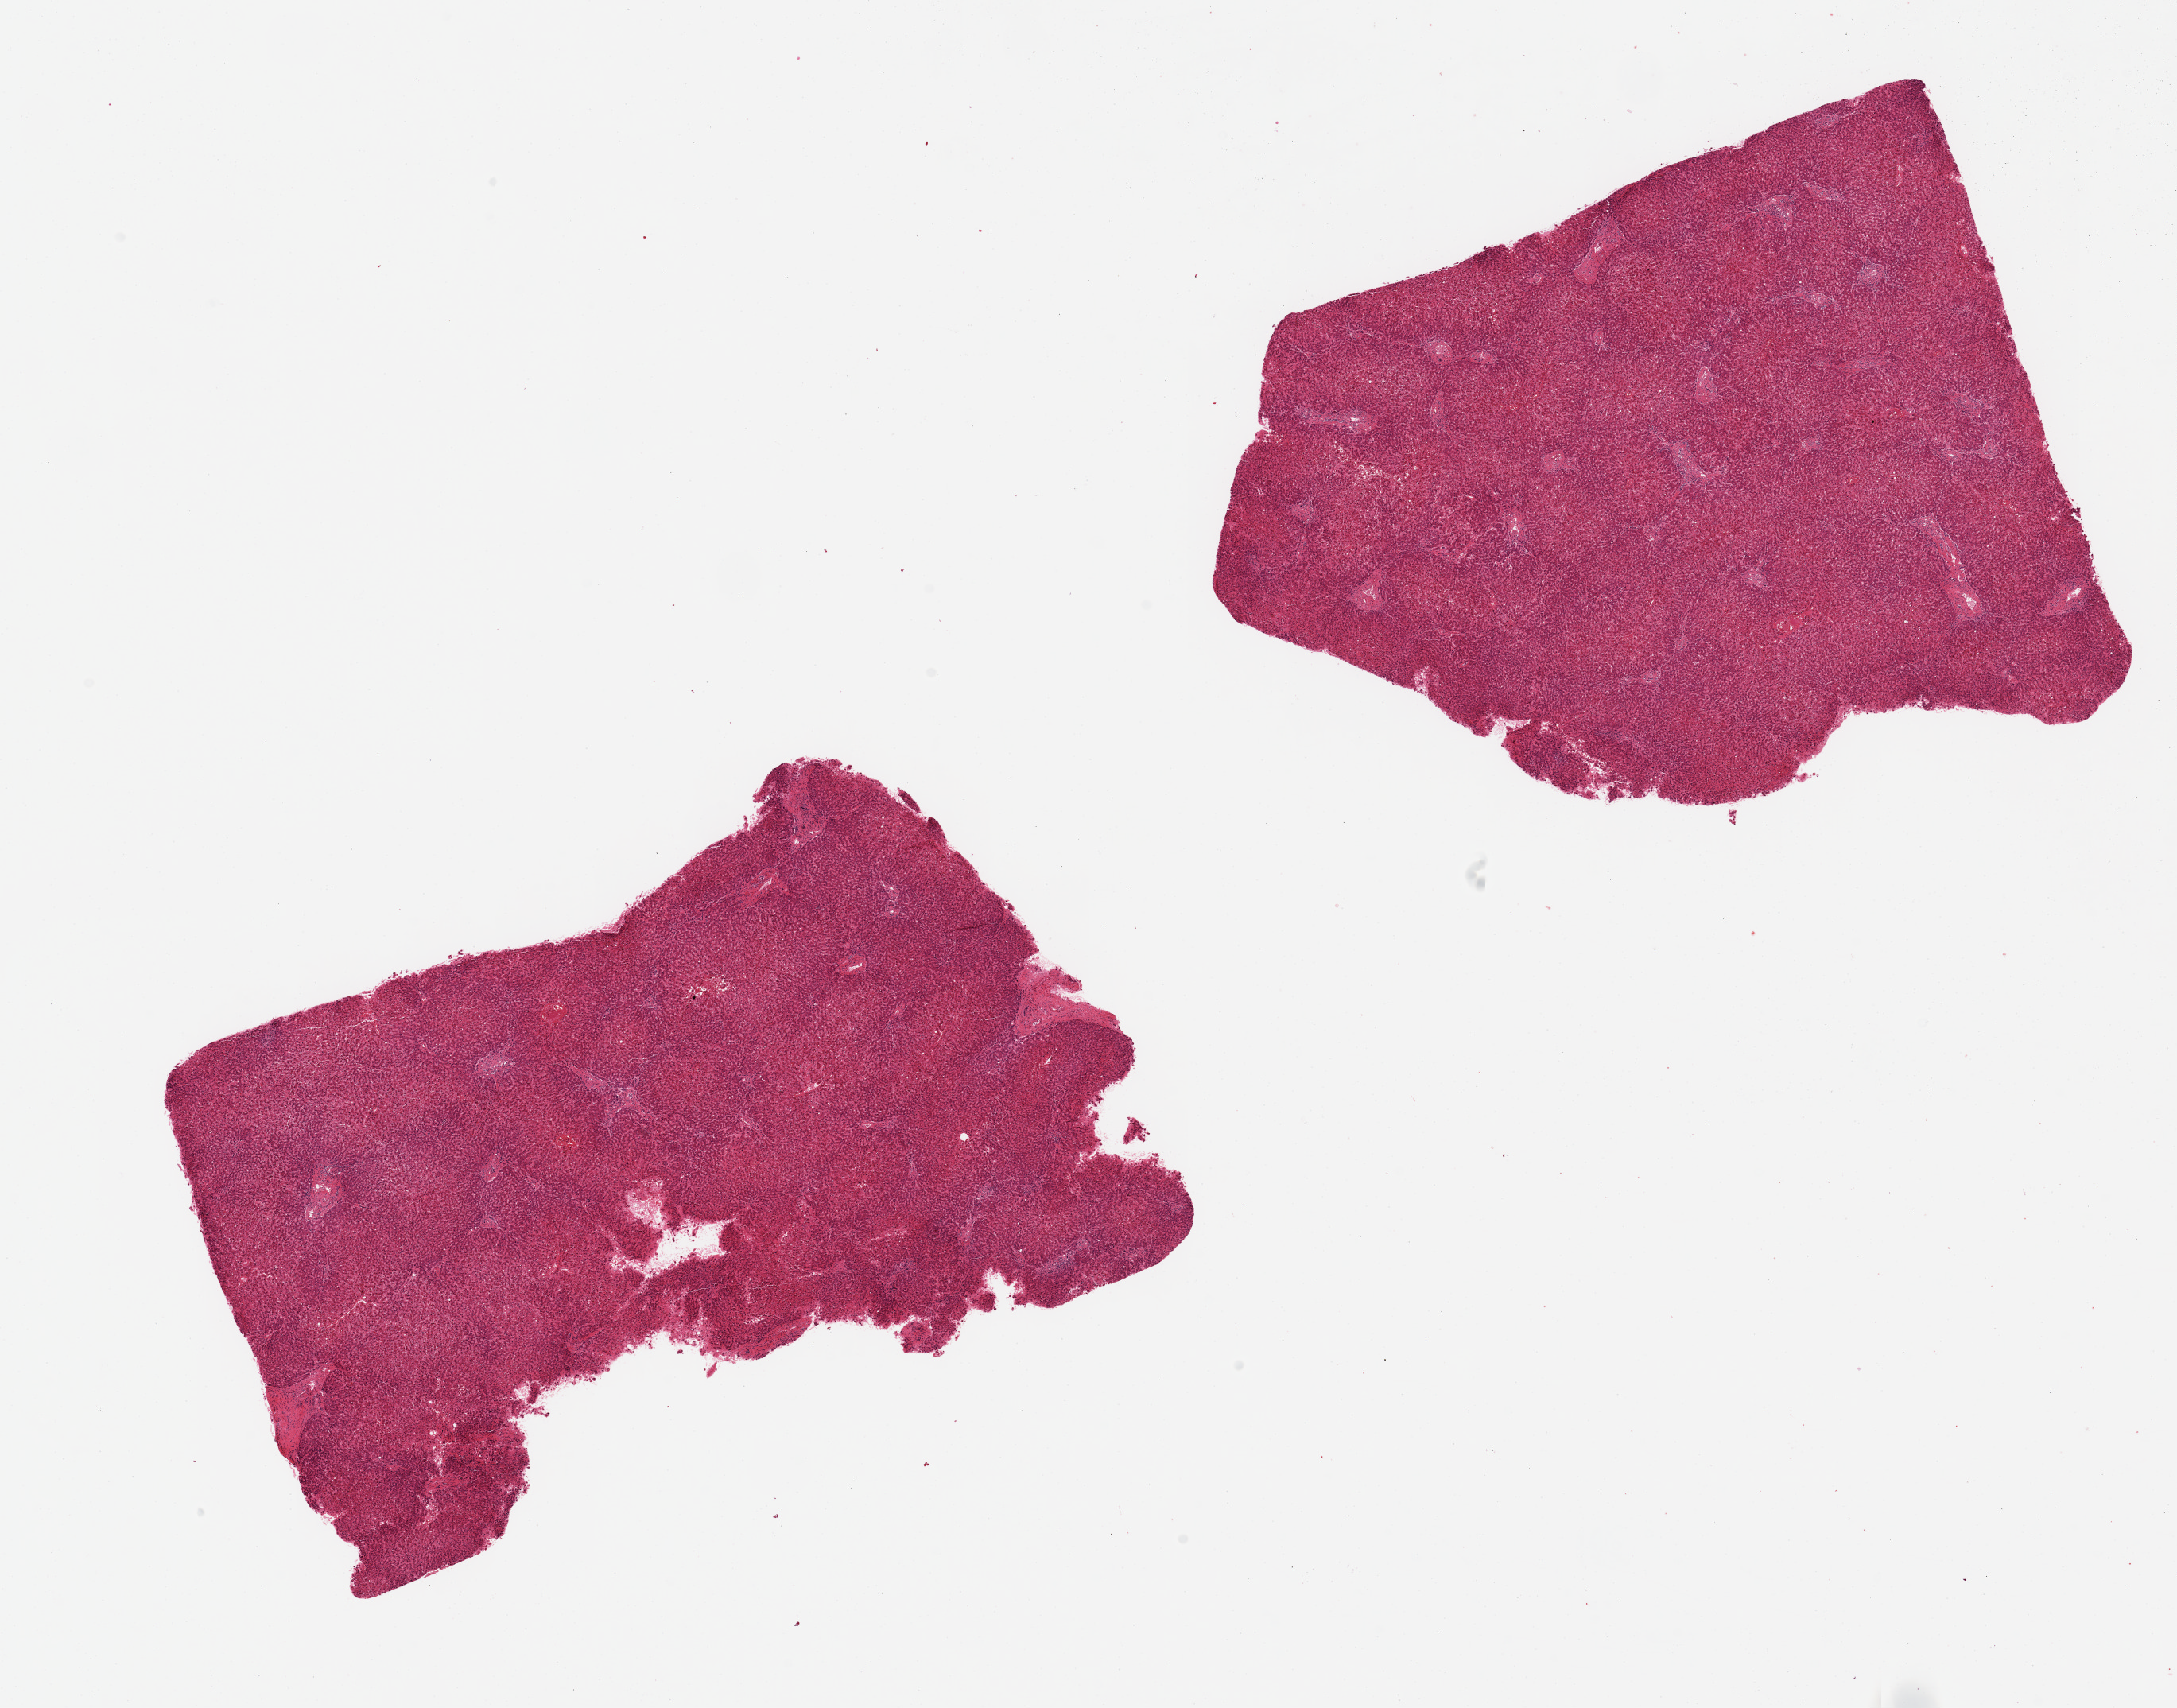
Whole-slide image, hematoxylin and eosin (H&E) stain — low-resolution overview of the scanned area, about 21.7 x 17.0 mm; PAXgene-fixed, paraffin-embedded tissue; section of liver (target tissue); tissue donor sample. Donor: male.
Review note (as recorded): 2 aliquots, ~7.5x5mm, diffuse microvesicular steatosis, possible mild chronic hepatitis, but portal tracts badly autolyzed, compromising assessment.